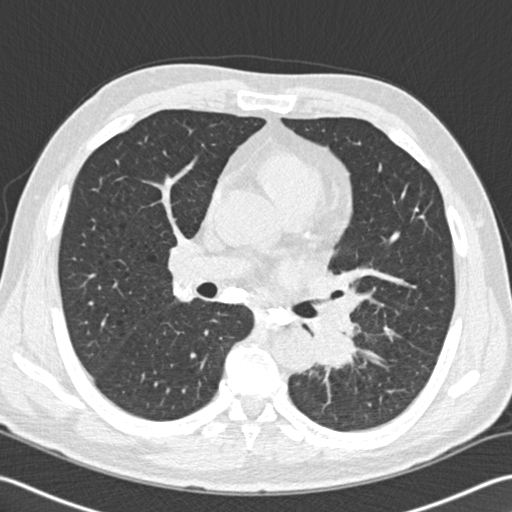
Low-dose screening chest CT, one axial slice. Position 97 of 170 along the scan axis. 120 kVp. Lung window (W 1500 / L -600 HU). 2 mm slice thickness. 512 × 512 image matrix, field of view 350 × 350 mm.
Structures marked on this image (outlined manually by an expert reader):
- lesion 1 (tumor, lower lobe of left lung): bounding box (x1, y1, x2, y2) in pixels: (317, 313, 355, 369)